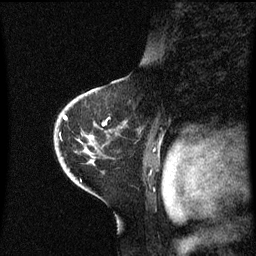
Breast MRI (dynamic contrast-enhanced), one sagittal slice. Slice 40 of 60 in the series (ordered by position). Dynamic contrast-enhanced series, image 2 of 3 at this slice position (ordered by acquisition). 1.5 T. TE 4.2 ms, TR 8.4 ms. 2.3 mm slice thickness. 256 × 256 image matrix. Patient: female, 46 years. From the clinical record (not read from this slice): setting: breast cancer imaged before/during neoadjuvant chemotherapy; receptor status: HER2-positive.
Annotated regions visible in this slice (semi-automatic segmentation, software-assisted and operator-edited):
- analysis volume of interest (the breast-tissue region the enhancement analysis was run in; not a lesion): bounding box [x1, y1, x2, y2] px = [54, 88, 127, 171]
- tumour enhancement mask (voxels above the 70 % enhancement threshold inside the analysis volume of interest): [64, 116, 67, 121]